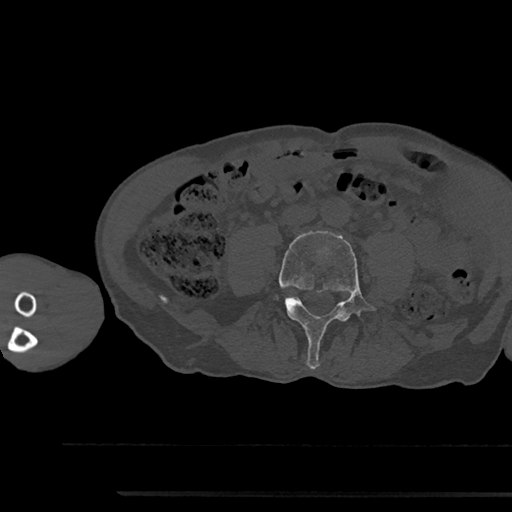
CT including the spine, one axial slice. Position 410 of 797 along the scan axis. Reconstruction kernel Br40s/3. Bone window (W 1800 / L 400 HU). 512 × 512 image matrix, field of view 367 × 367 mm. Patient: male, 79 years. Case-level facts recorded for this patient, not image findings: primary cancer: prostate.
Outlined on this slice (semi-automatically segmented with operator editing):
- L4 vertebra: bounding box (x1, y1, x2, y2) in pixels: (277, 231, 377, 369)